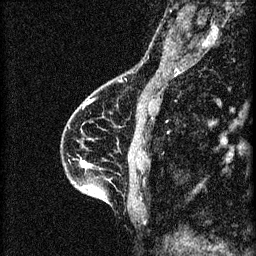
Breast MRI (dynamic contrast-enhanced), one sagittal slice. Slice 22 of 60 in the series (ordered by position). 3 images stored at this slice position (order not interpretable as contrast timing). 1.5 T. TE 4.2 ms, TR 8.2 ms. 2 mm slice thickness. 256 × 256 image matrix, field of view 180 × 180 mm. Patient: female, 46 years.
Annotated regions visible in this slice (semi-automatic segmentation, software-assisted and operator-edited):
- analysis volume of interest (the breast-tissue region the enhancement analysis was run in; not a lesion): box from (x=61, y=114) to (x=148, y=209) px
- tumour enhancement mask (voxels above the 70 % enhancement threshold inside the analysis volume of interest): (x=81, y=160)–(x=91, y=189)